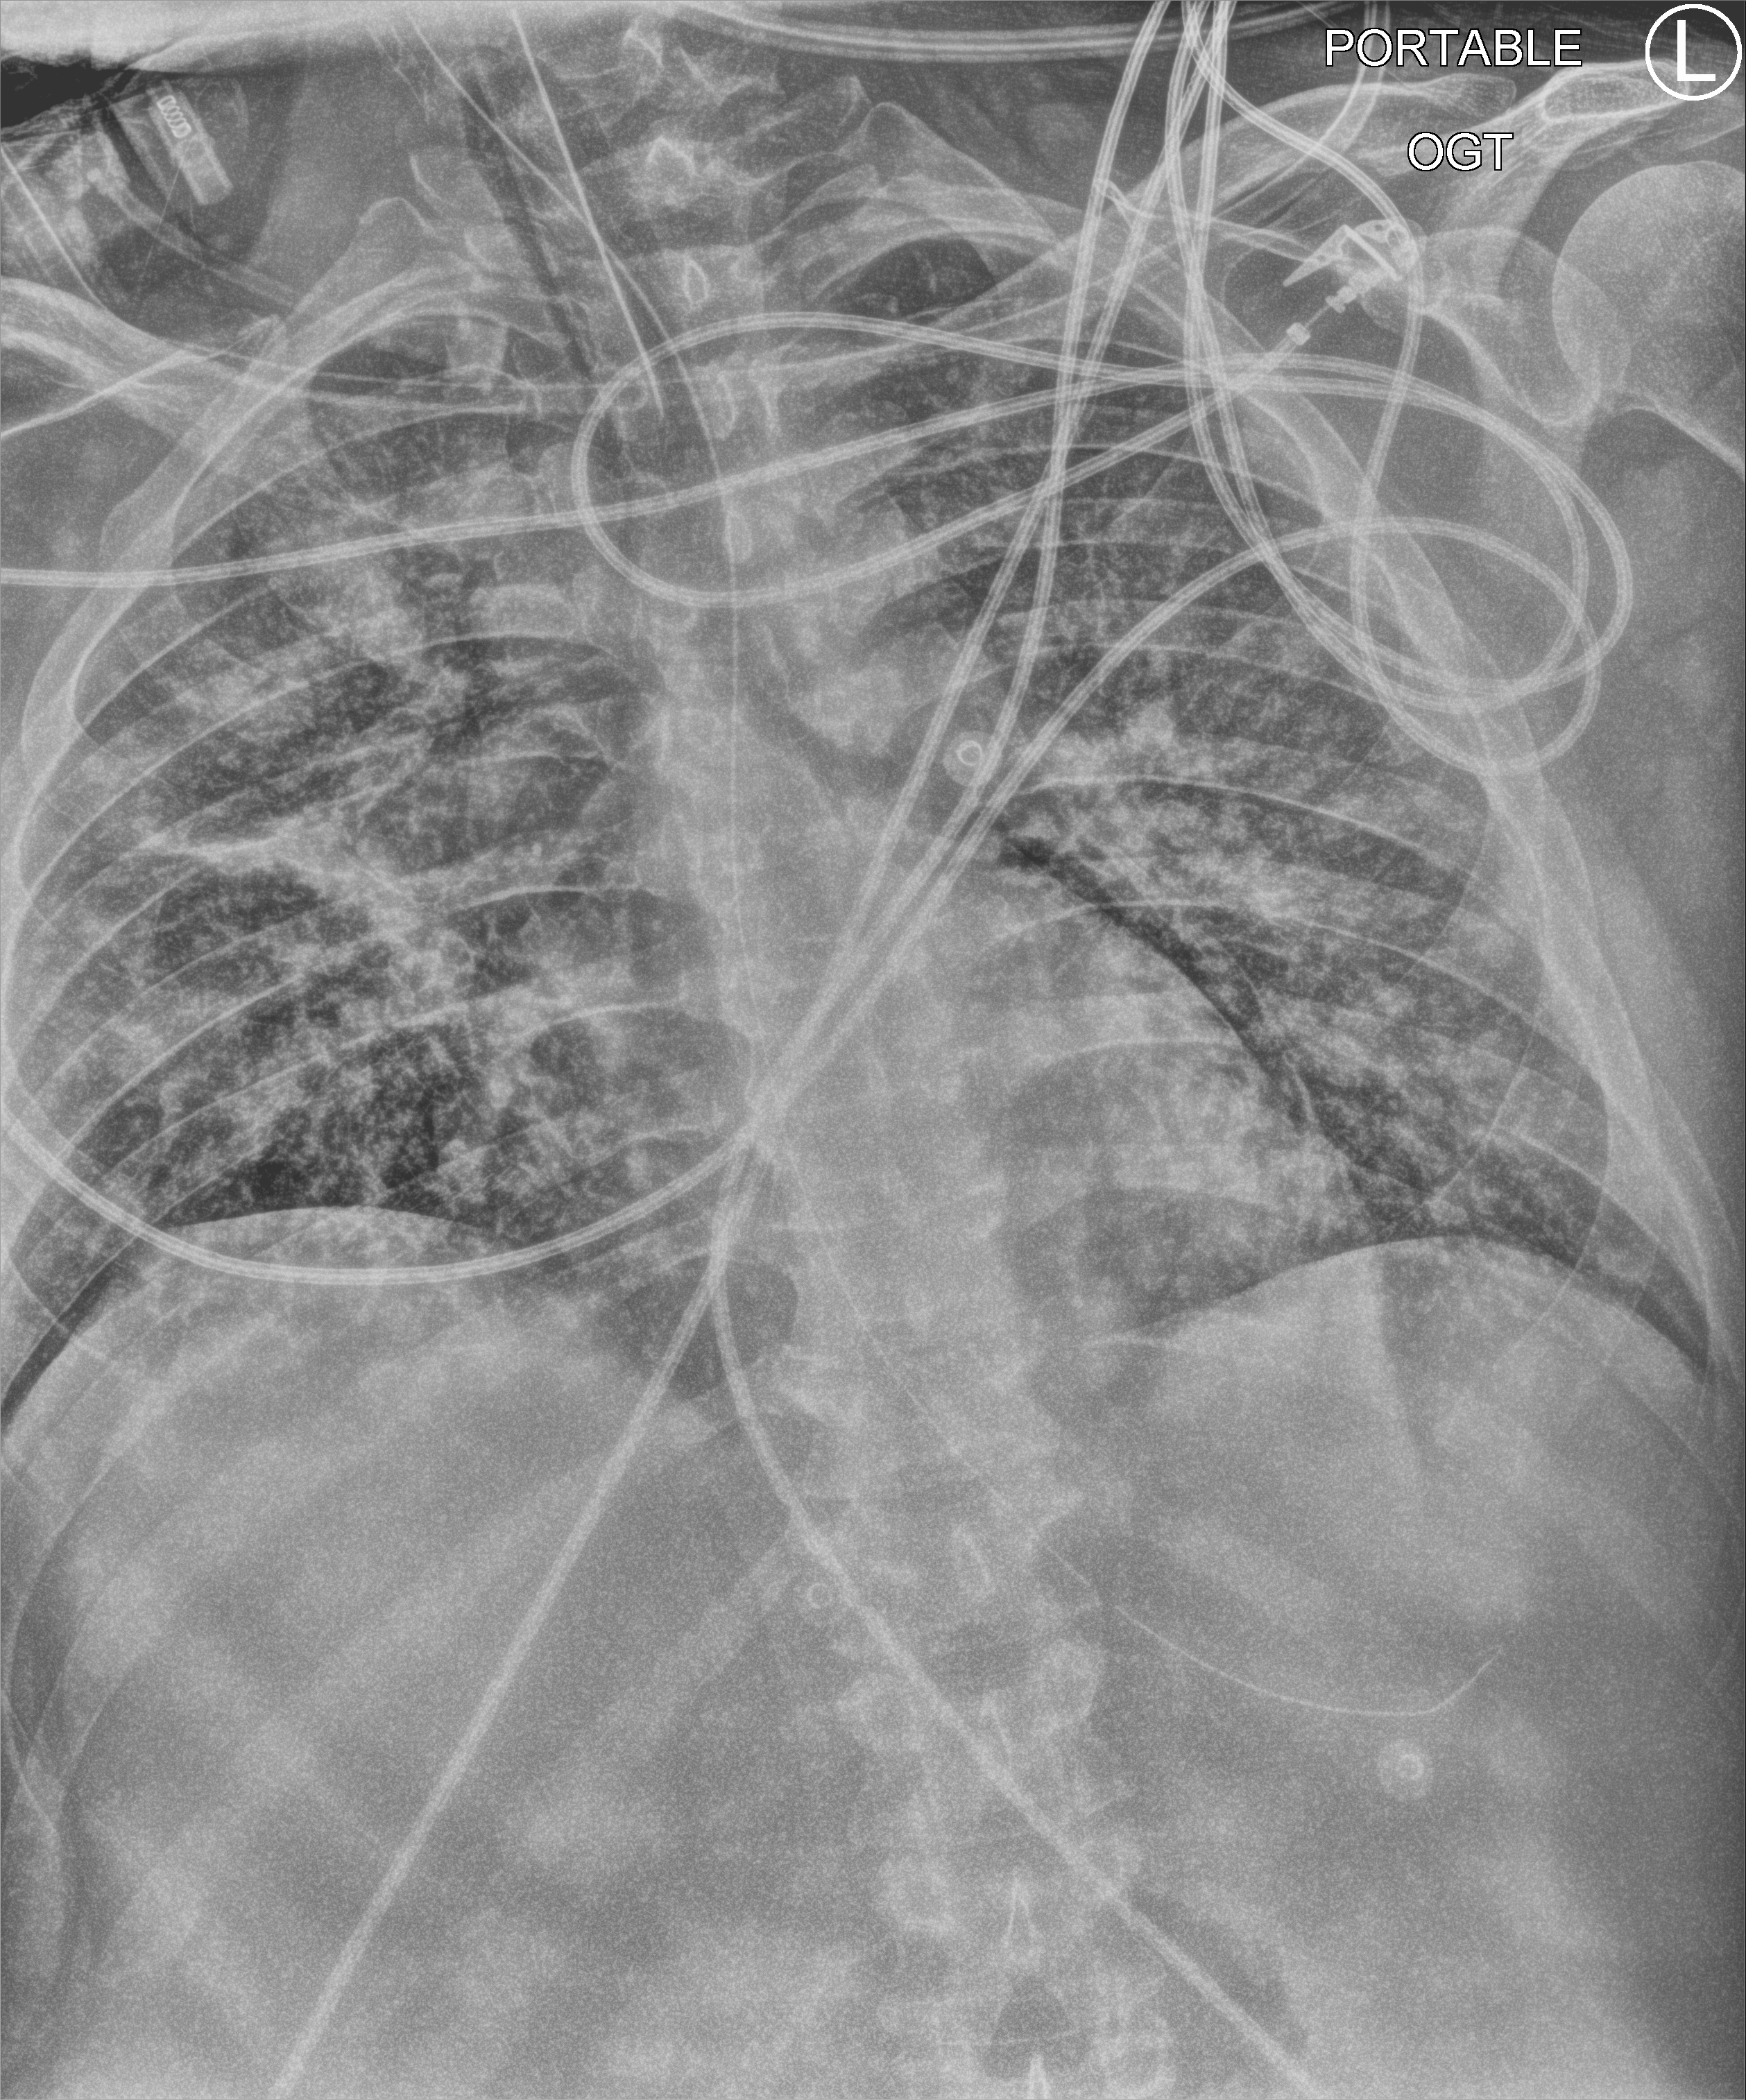
Bedside chest radiograph (computed radiography), anteroposterior (AP) projection. Adult patient hospitalised with COVID-19, age 18–59 years.
From the hospital-stay record, not from the radiograph (when in the stay this image was taken is not recorded): admitted to intensive care during this hospital stay: yes; mechanically ventilated during this hospital stay: yes.